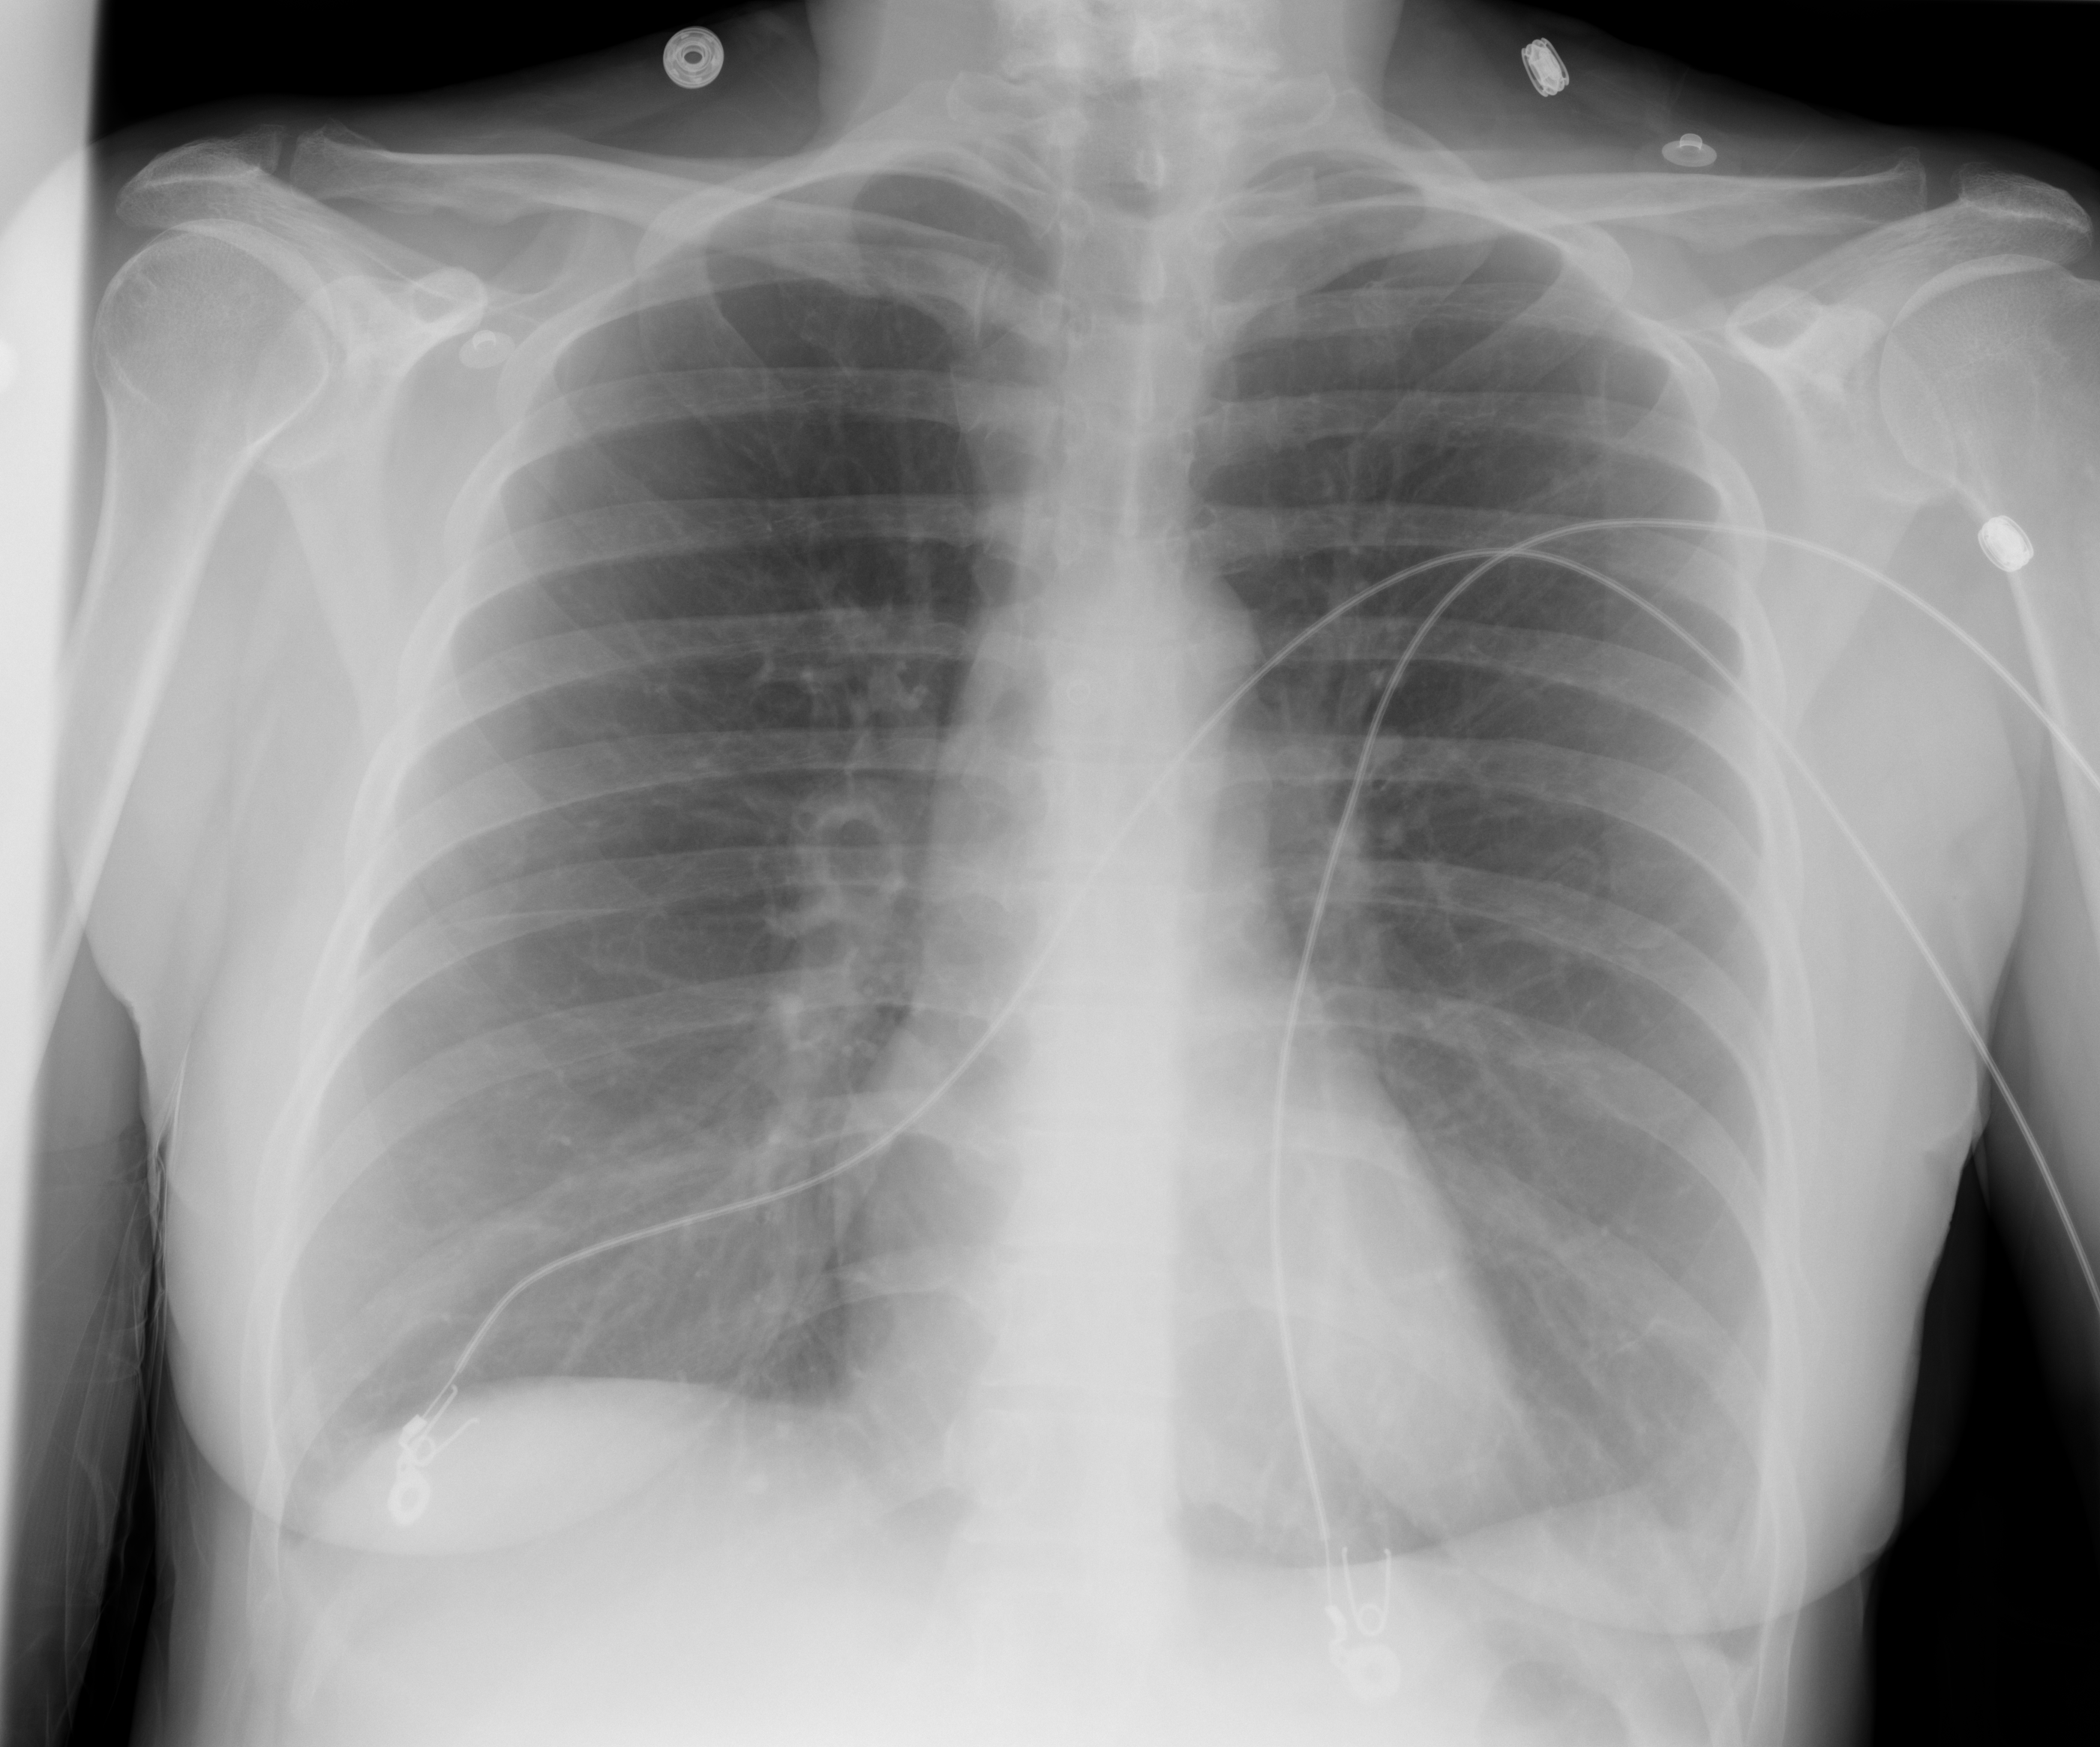
Chest X-ray (portable), AP projection. Female patient, age 47 years; imaged 0 days after the COVID-19 diagnosis.
Radiologist's key findings for this exam: Lungs are well inflated and clear.